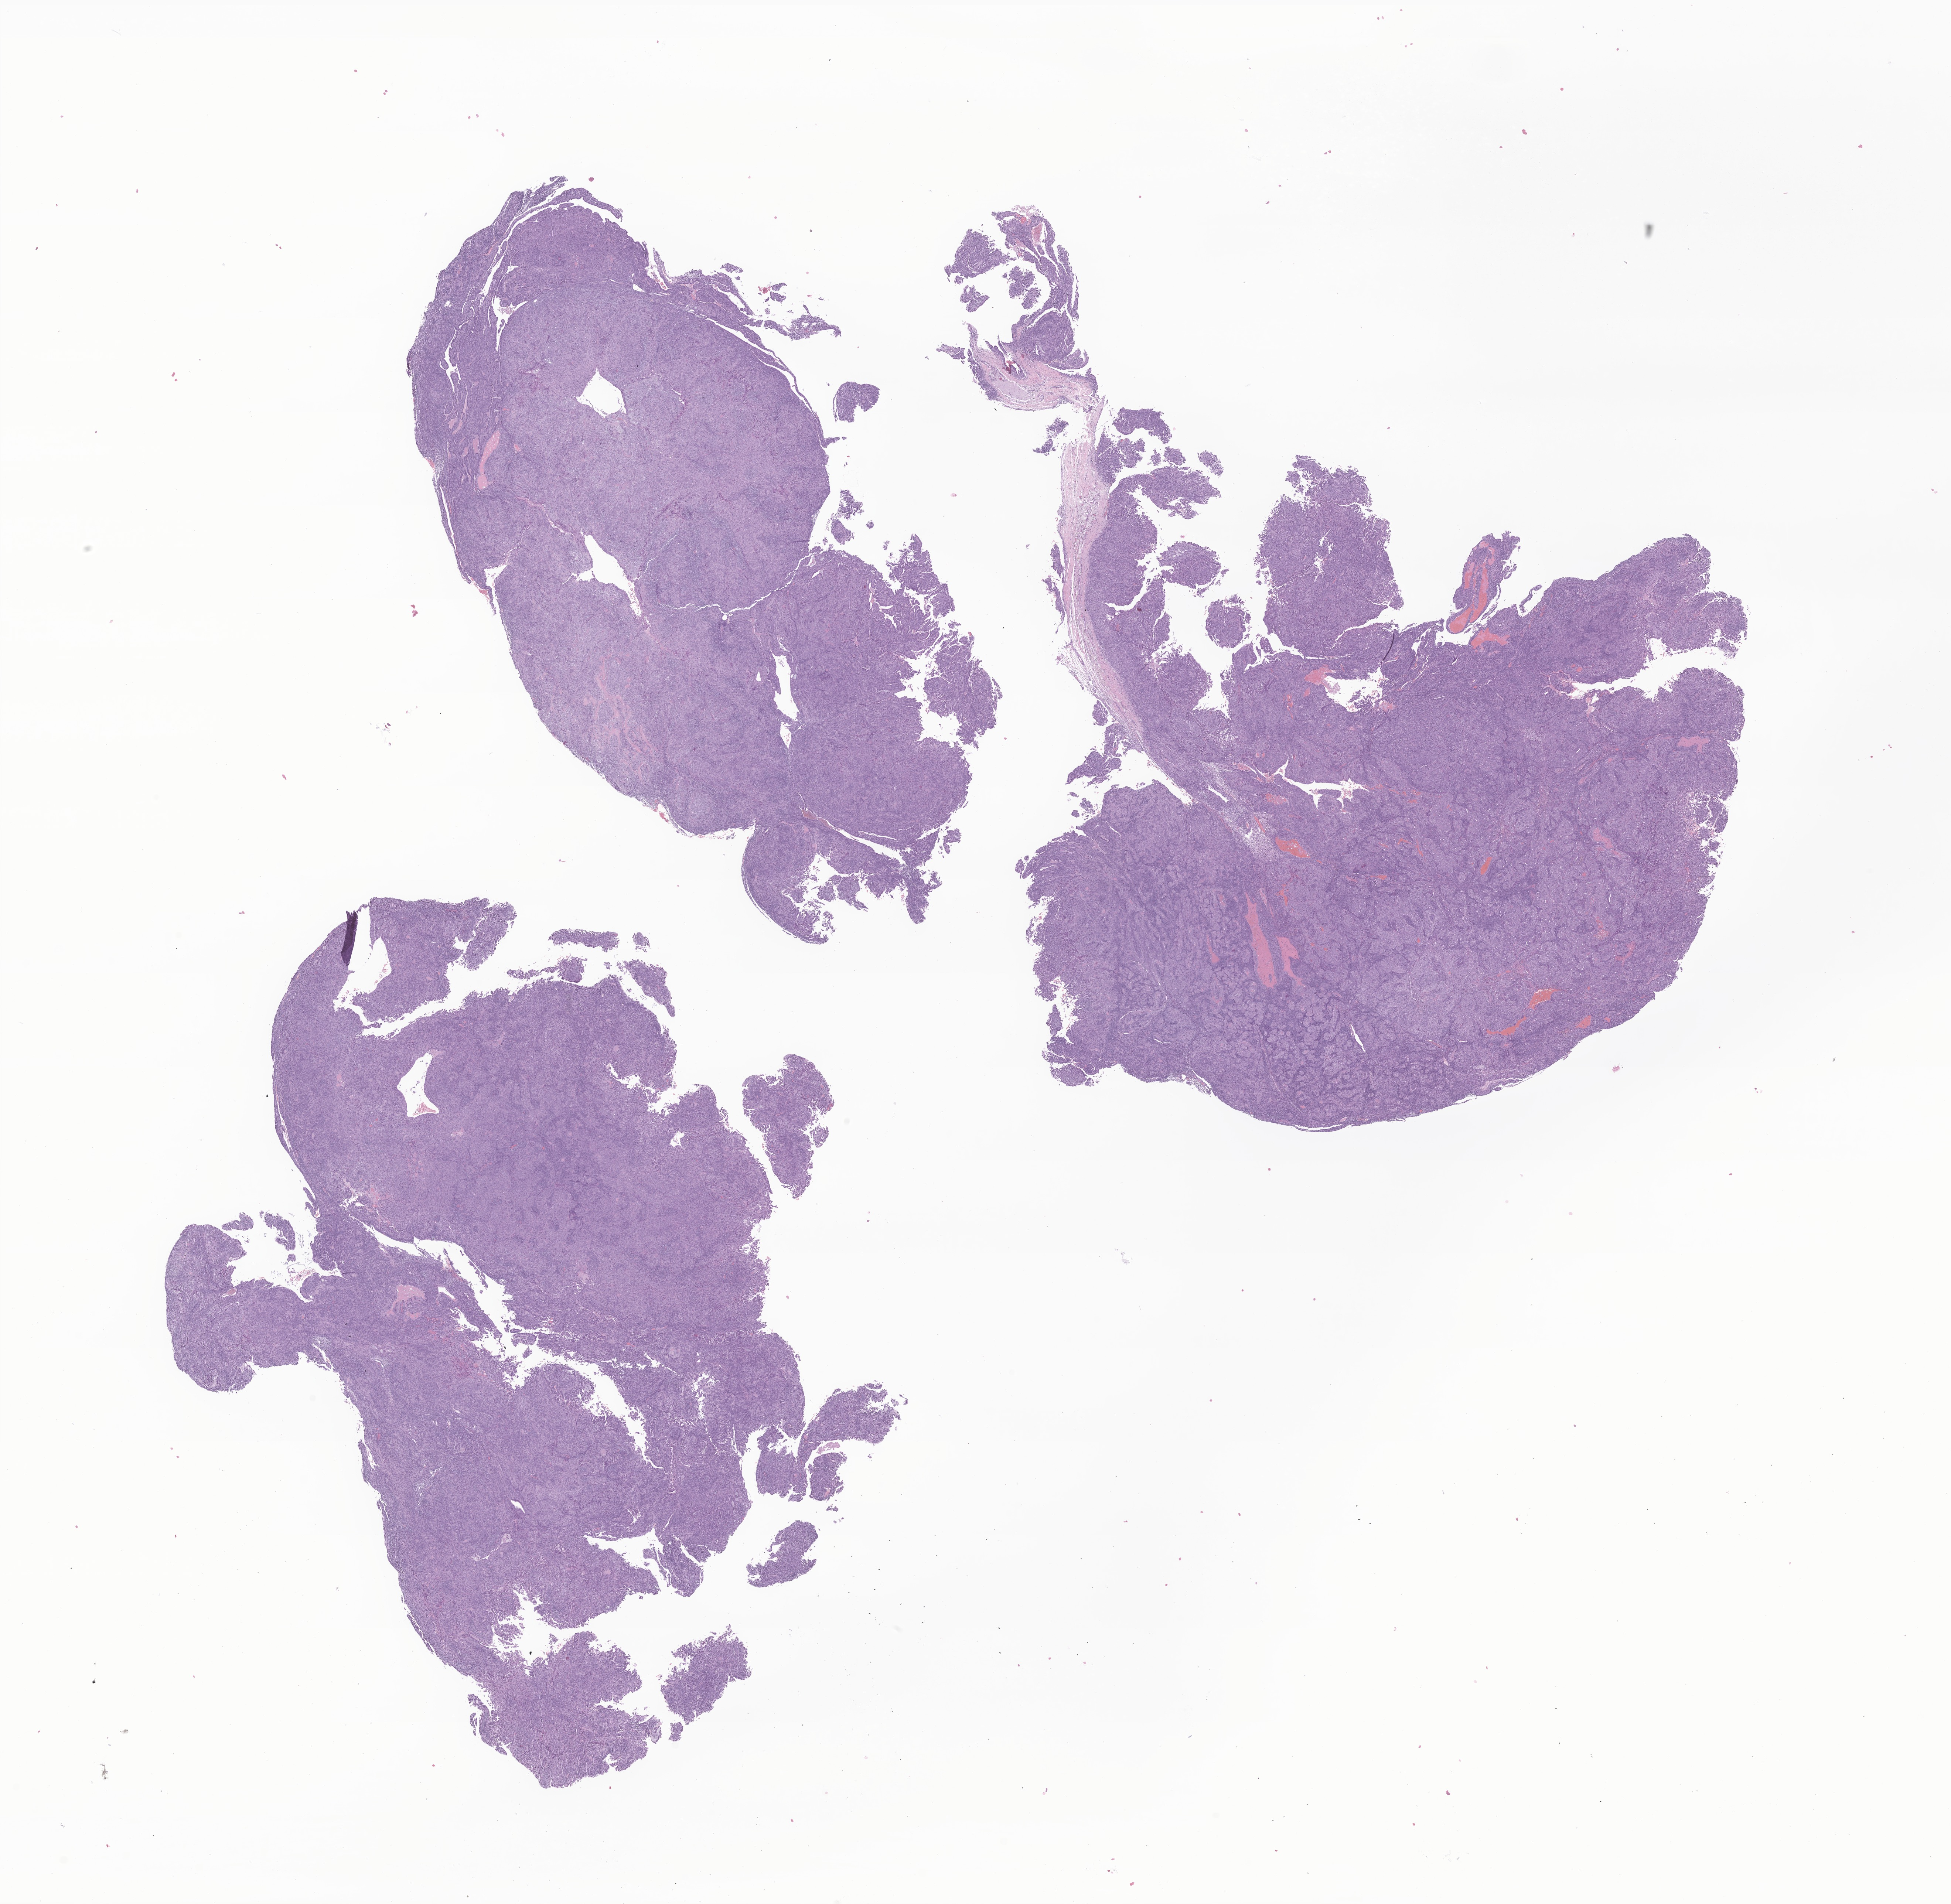
Hematoxylin and eosin (H&E) whole-slide image of tumor tissue from the soft tissue of abdomen, whole scanned area (about 22.3 x 21.7 mm) shown as a low-resolution overview, FFPE section. Patient: female, age 184 months (15 years 4 months).
Diagnosis: Synovial sarcoma, NOS.